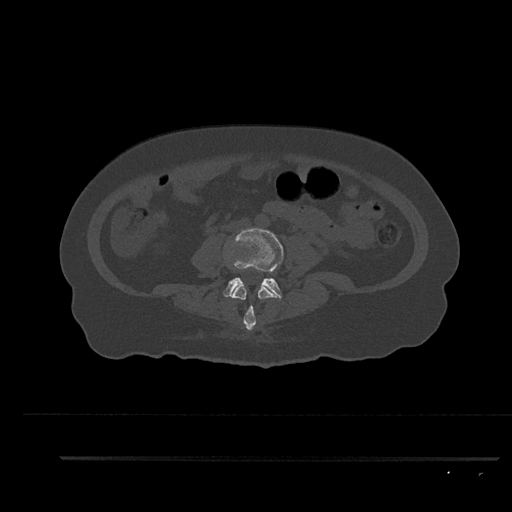
CT including the spine, one axial slice; slice 48 of 797 in the series (ordered by position); reconstruction kernel Br40s/3; bone window (W 1800 / L 400 HU); 0.5 mm slice thickness; 512 × 512 image matrix, field of view 408 × 408 mm. Female patient, age 44 years. From the clinical record (not read from this slice): primary cancer: renal; vertebrae with lytic lesions (as recorded): L1.
Annotated regions visible in this slice (semi-automatic segmentation, software-assisted and operator-edited):
- L3 vertebra: bounding box (x1, y1, x2, y2) in pixels: (231, 284, 281, 330)
- L4 vertebra: (223, 228, 284, 299)